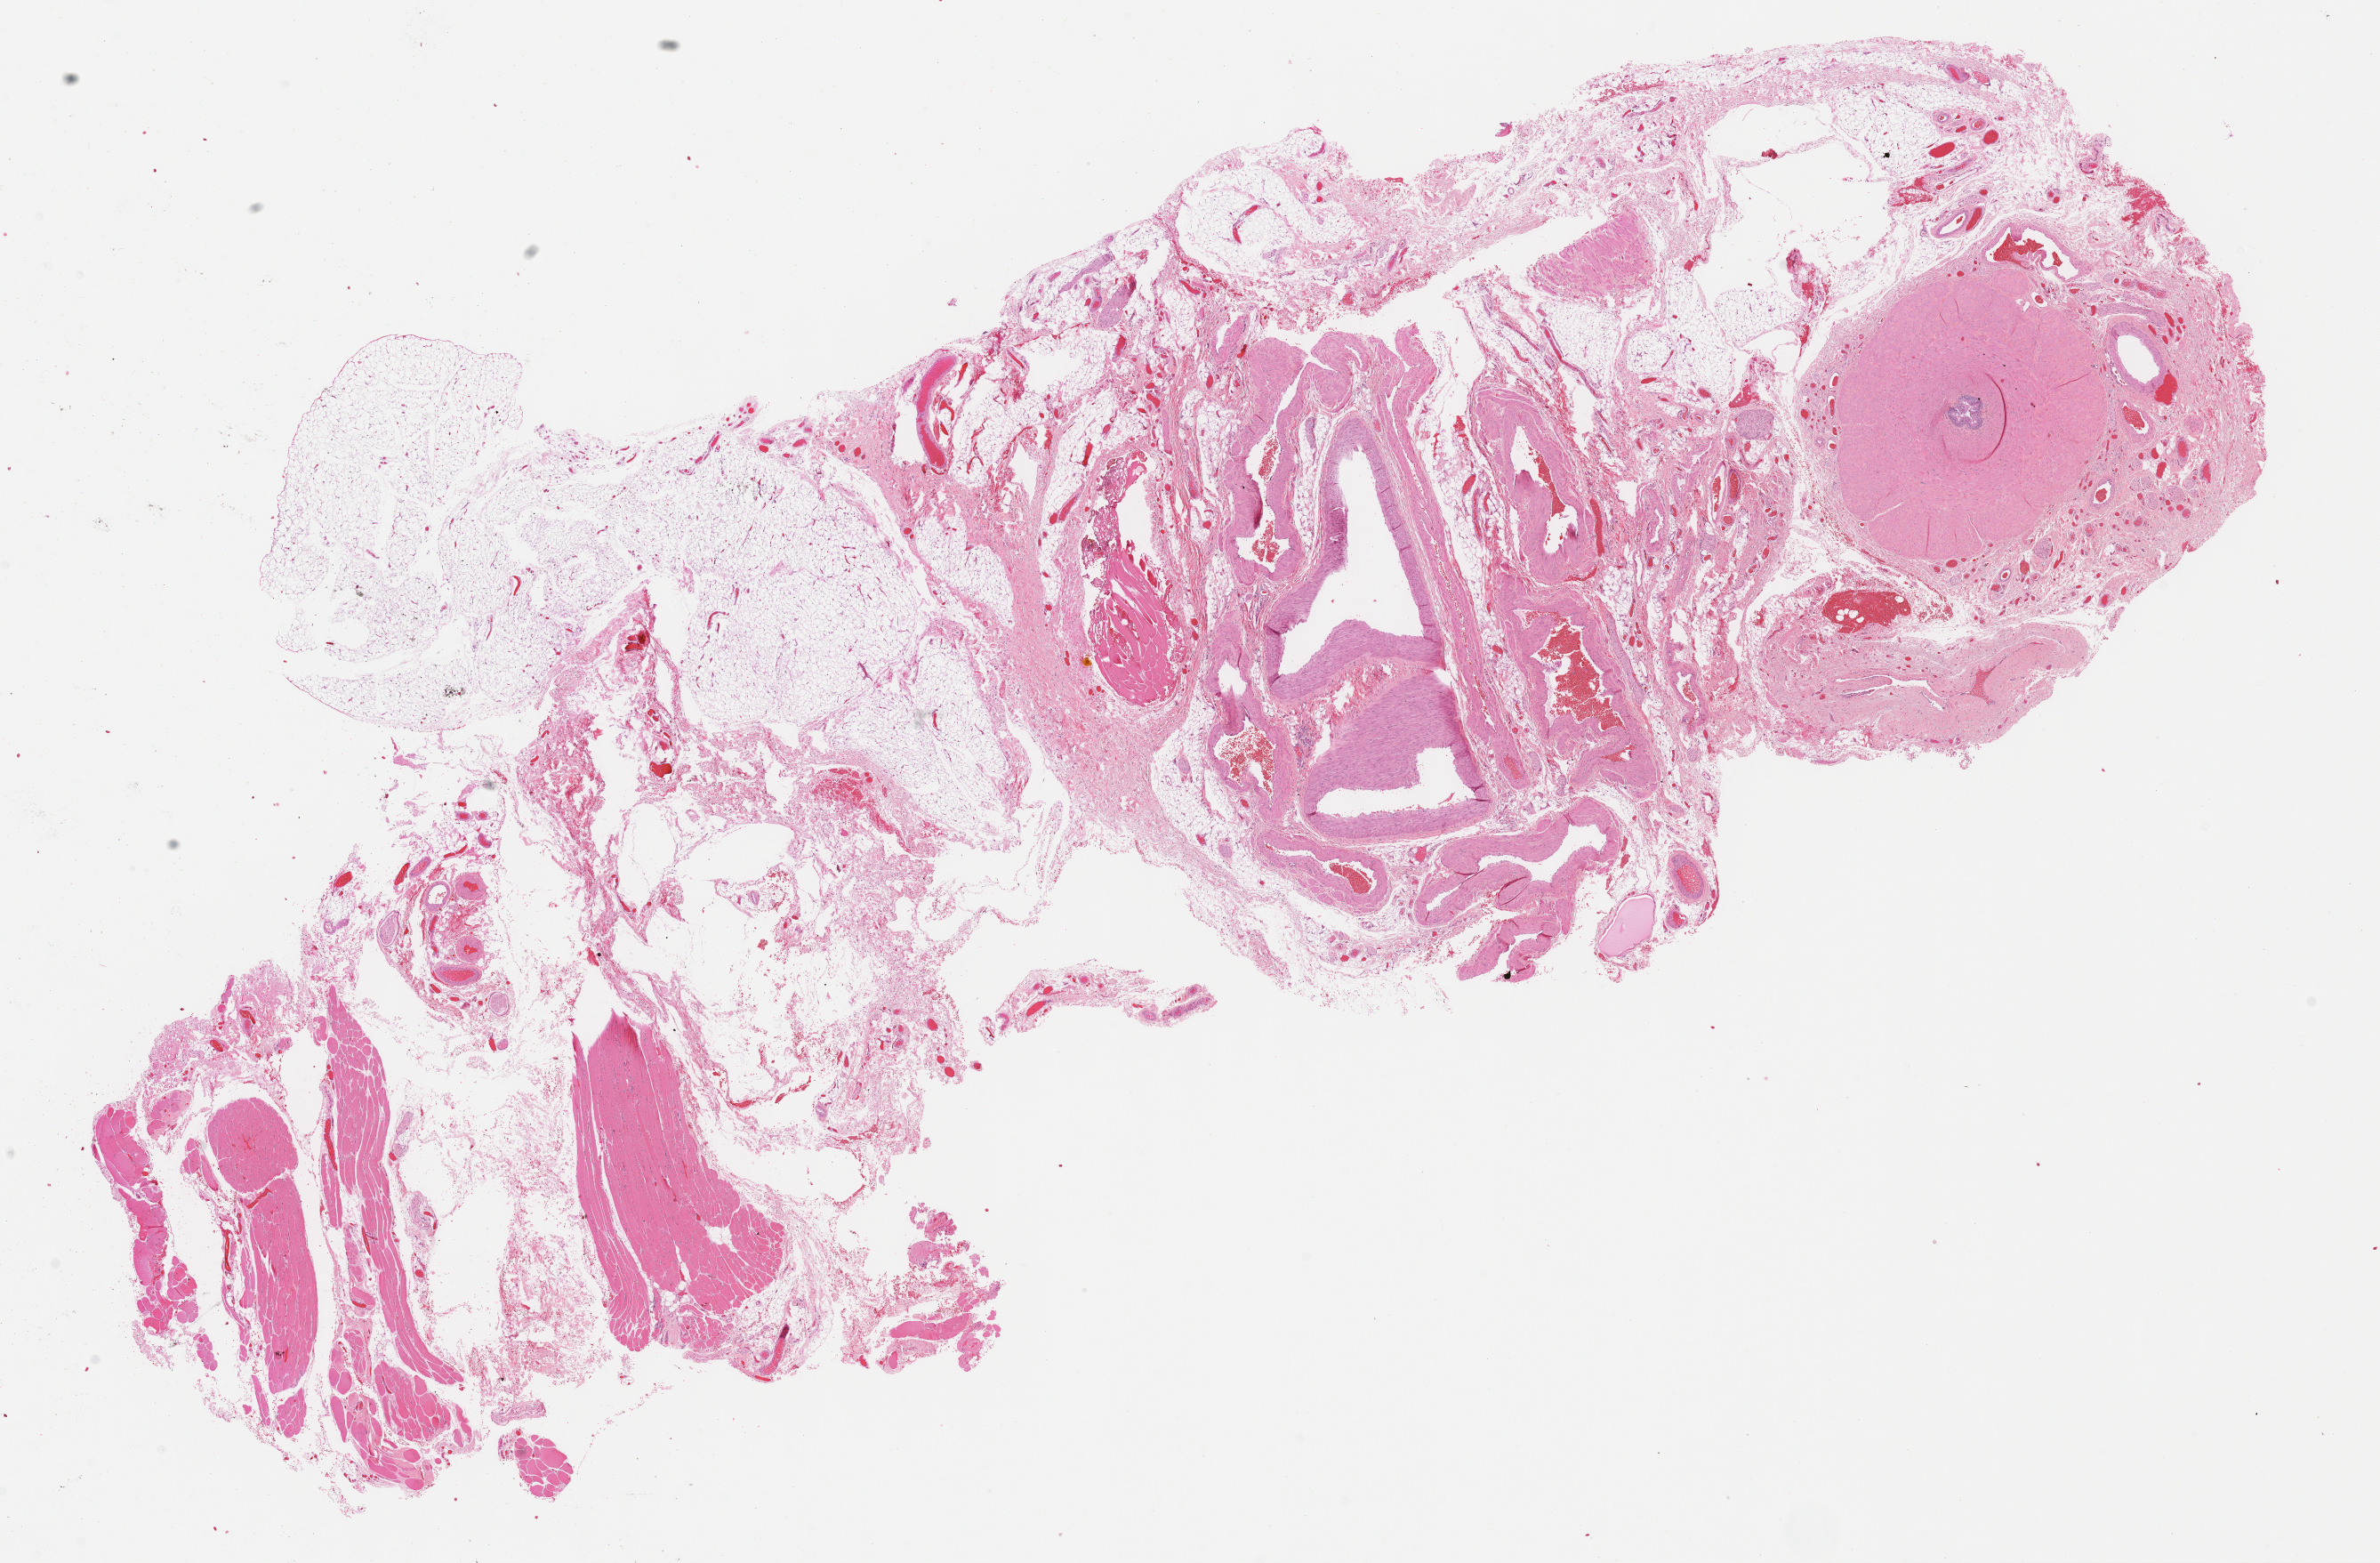
H&E whole-slide image — shown as a low-resolution overview of the whole scanned area (about 21.6 x 14.2 mm). Formalin-fixed paraffin-embedded (FFPE) diagnostic section. Sample: primary tumour, testis. Patient: male, age at initial diagnosis 38 years.
Histologic diagnosis: Seminoma, NOS. Laterality: left.